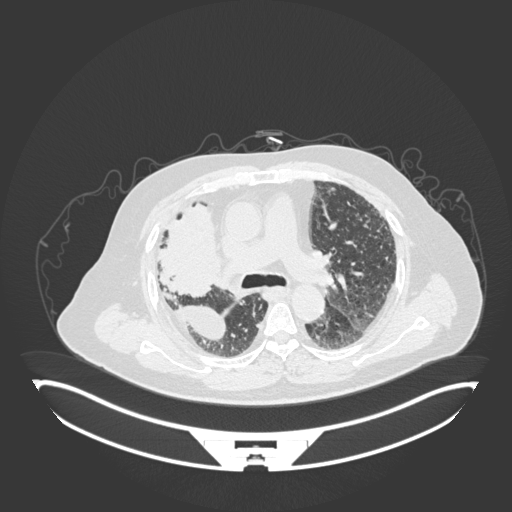
Chest CT, one axial slice. Position 109 of 201 along the scan axis. Reconstruction kernel B30f. Lung window (W 1500 / L -600 HU). 1 mm slice thickness. 512 × 512 image matrix. Male patient, age 69 years. From the clinical record (not read from this slice): clinical TNM (as recorded): T4 N3 M1.
Outlined on this slice (rectangle marked by the reading radiologist):
- lung tumour (recorded histology: adenocarcinoma): bounding box (x1, y1, x2, y2) in pixels: (156, 202, 225, 297)